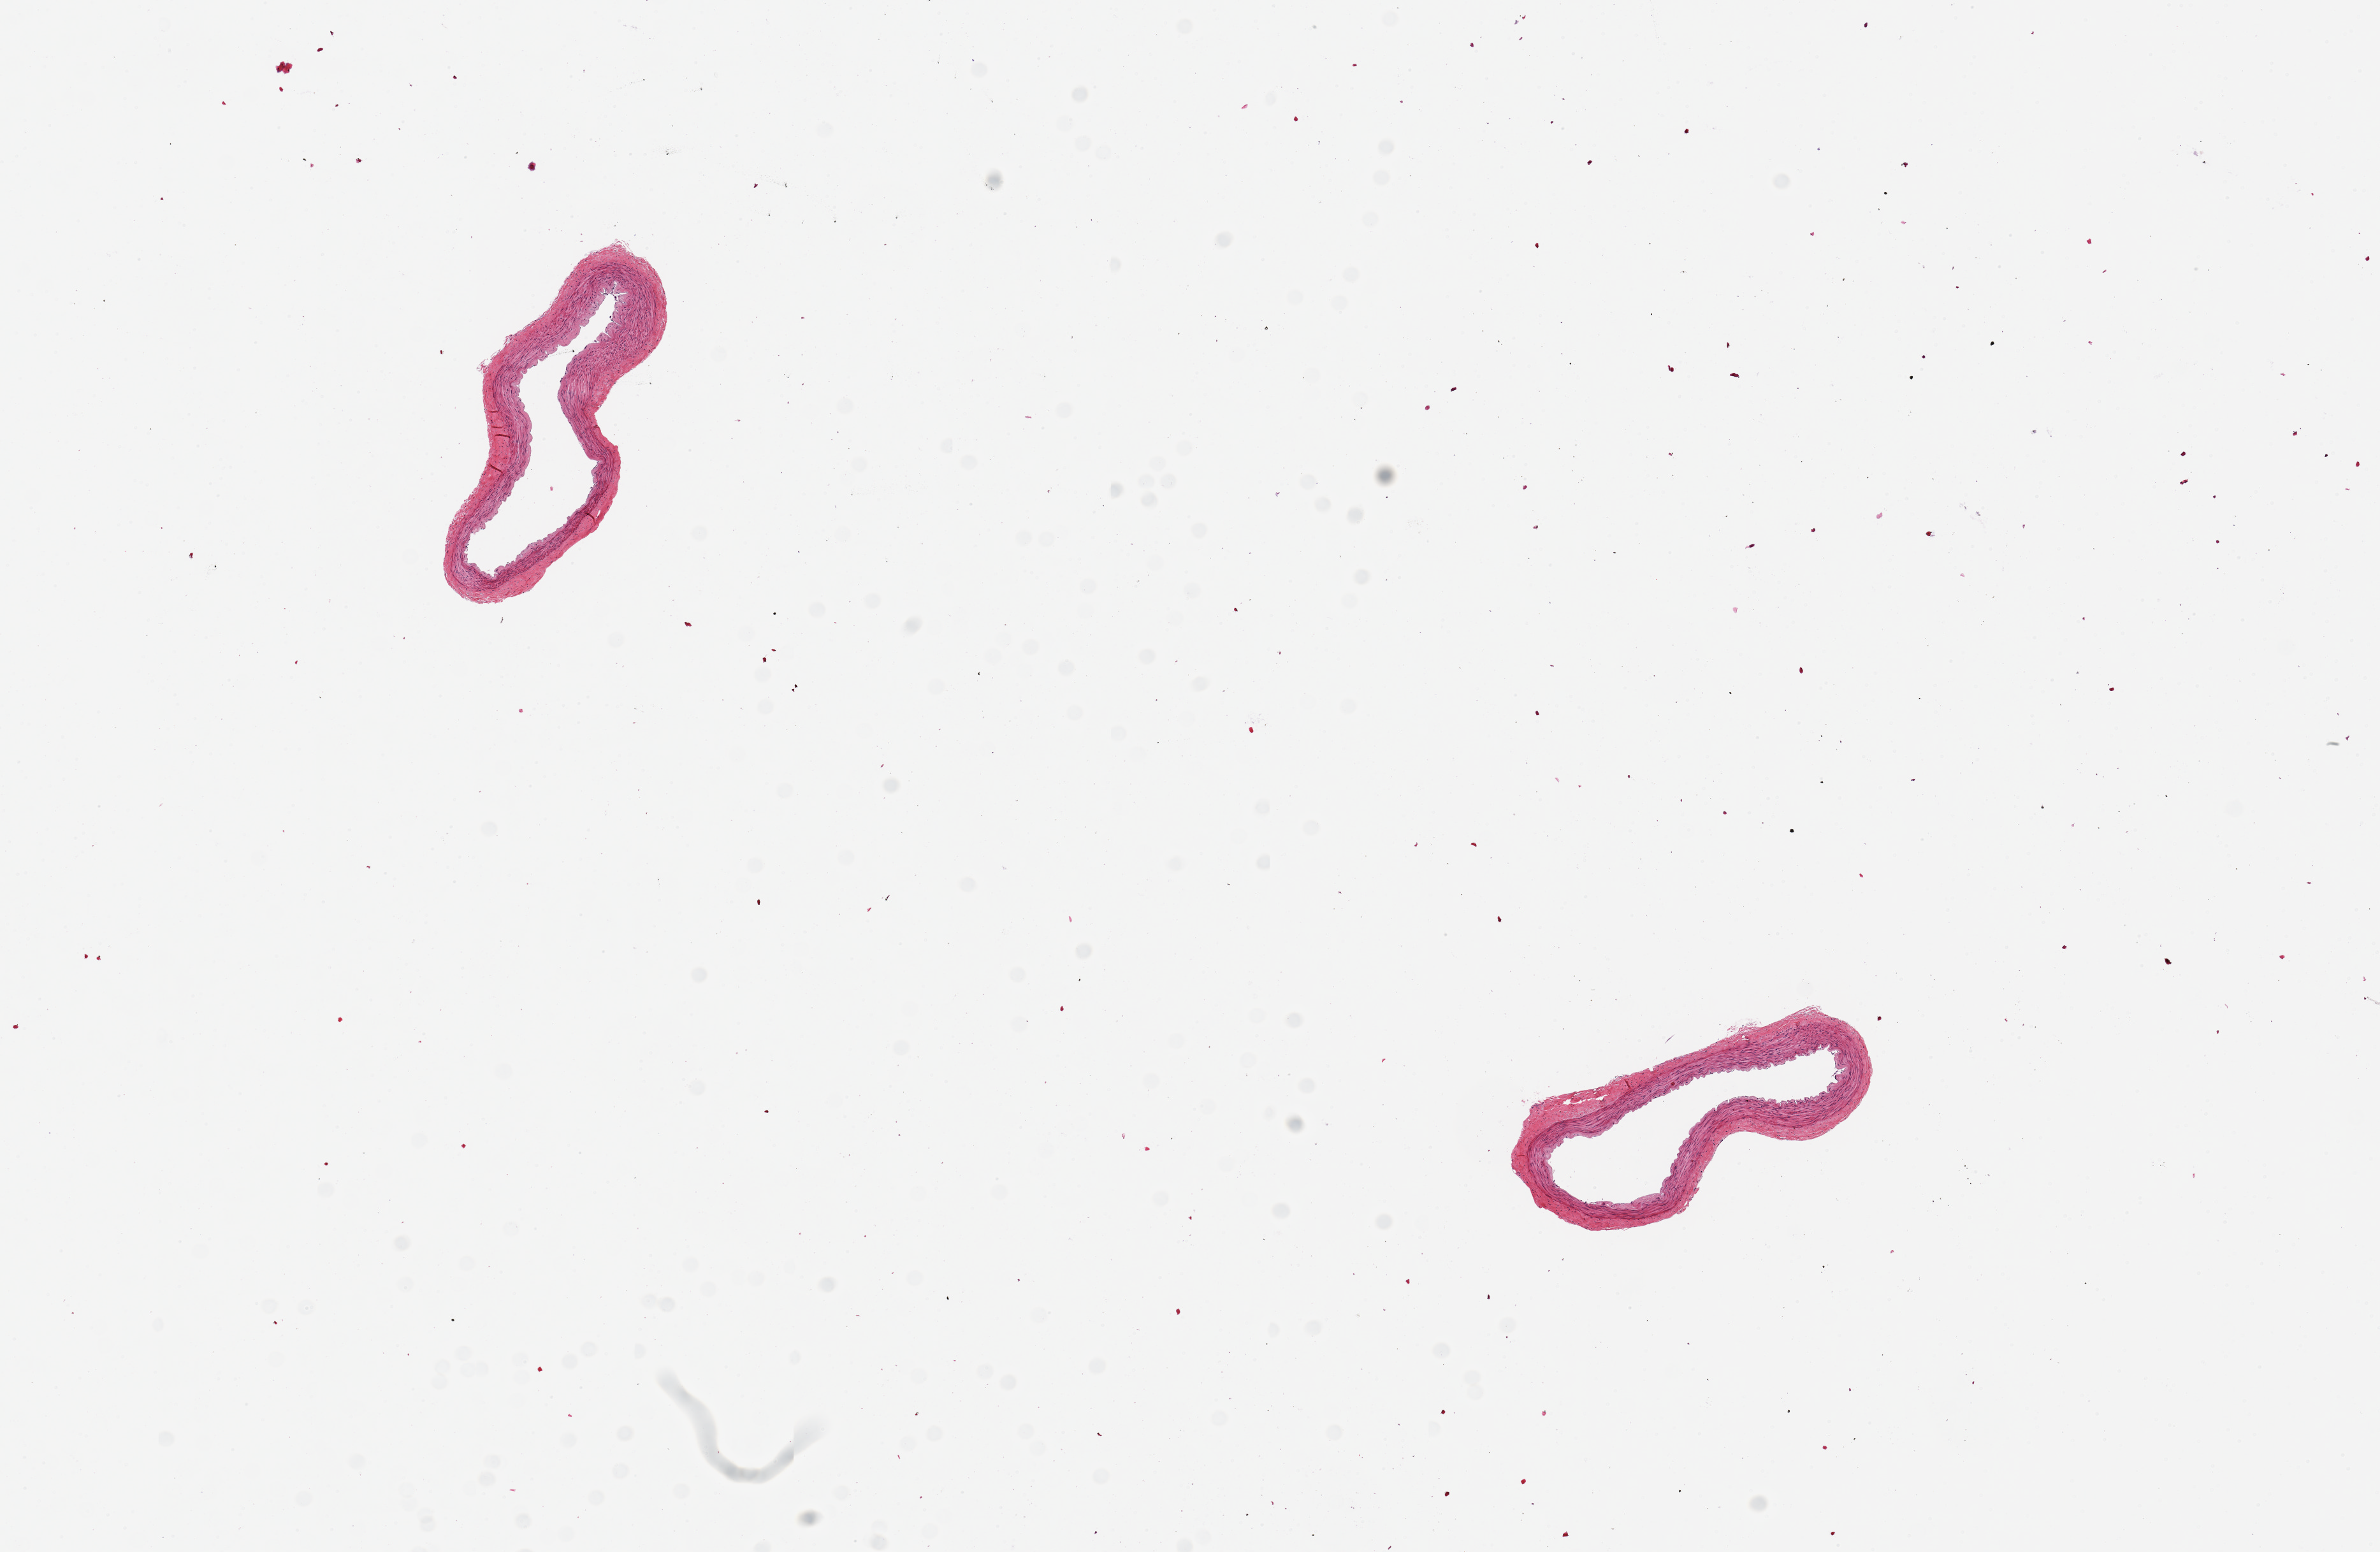
Whole-slide image, hematoxylin and eosin (H&E) stain, whole scanned area (about 14.8 x 9.6 mm, slide scanned at 20x) shown as a low-resolution overview; PAXgene-fixed paraffin-embedded (PFPE) section; target tissue: tibial artery; donor tissue sample. Donor sex: female.
• pathologist's review note for this sample: 2 pieces, 2x1 & 2x1mm; Delicate arteries; well dissected, no adipose